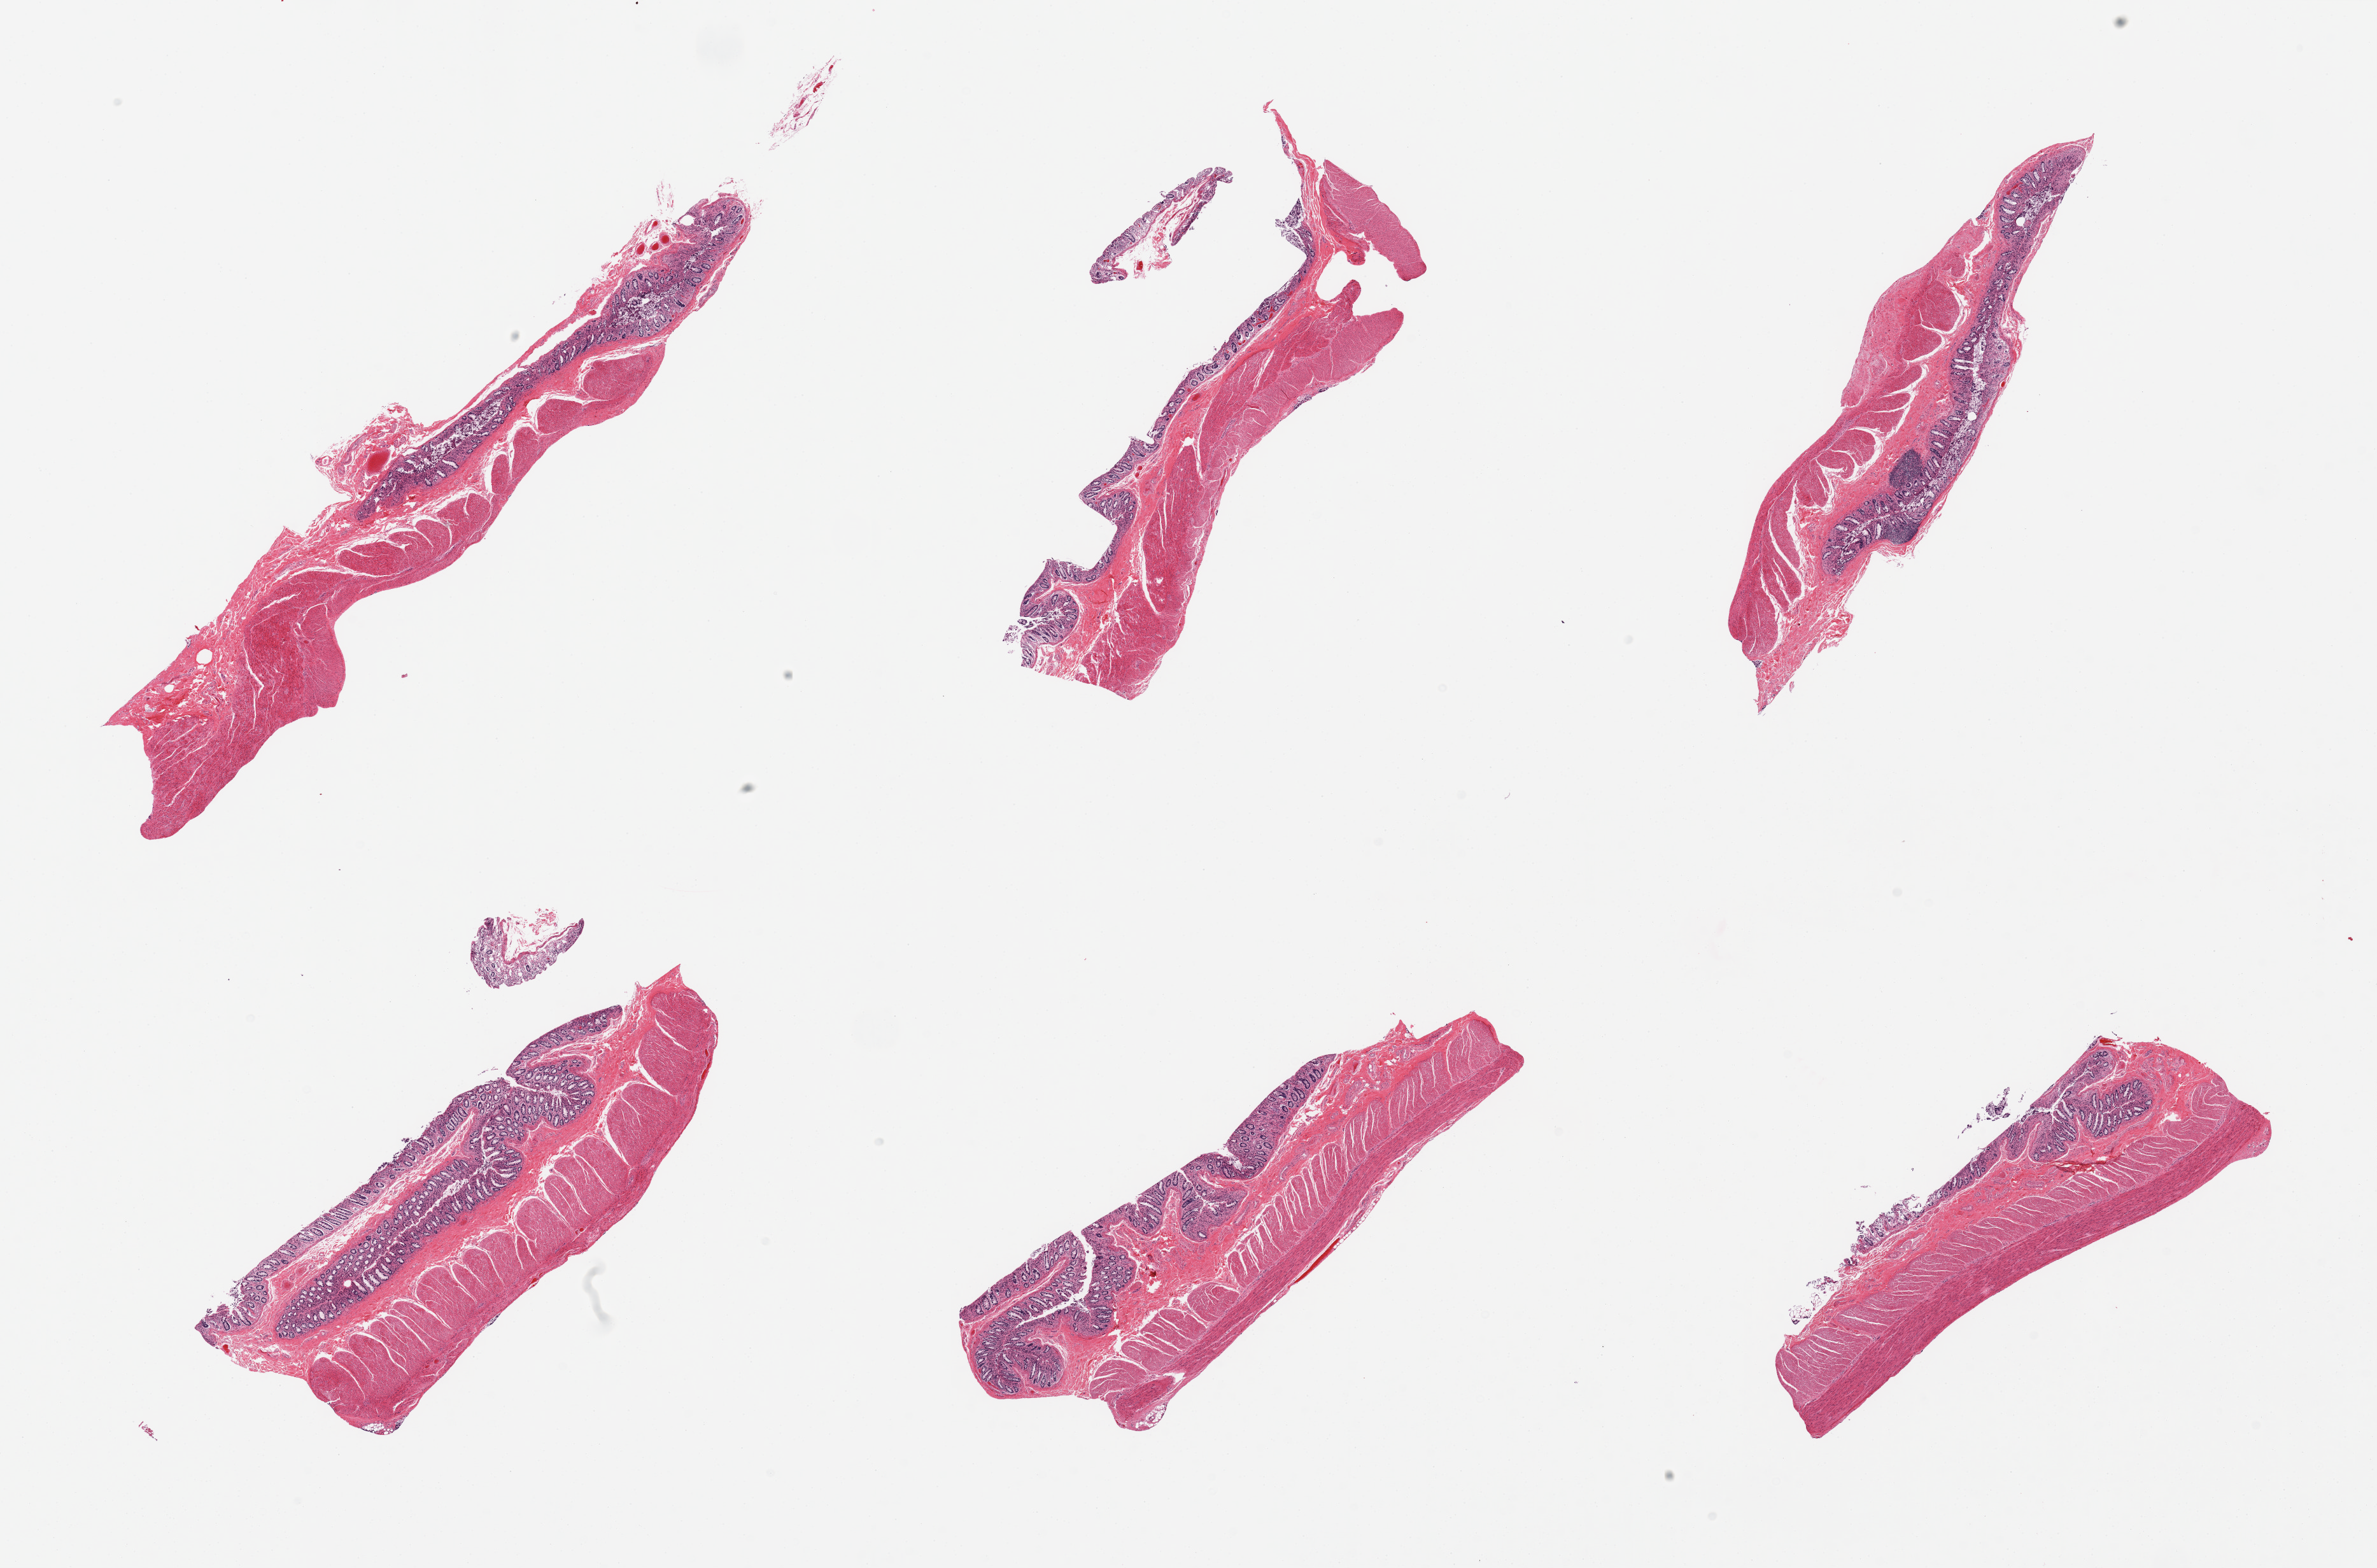
Whole-slide image, haematoxylin and eosin stain — low-resolution overview of the scanned area, about 29.5 x 19.5 mm. PAXgene-fixed, paraffin-embedded tissue. Target tissue: transverse colon. Donor tissue sample. Donor sex: male.
- pathologist's review note for this sample: 6 pieces, mucosa up to ~0.5mm, `15-20% thickness